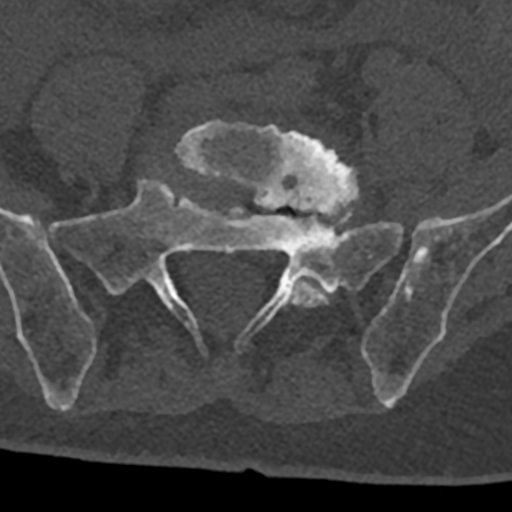
CT including the spine, one axial slice; slice 166 of 797 in the series (ordered by position); reconstruction kernel Br40s/3; 120 kVp; bone window (W 1800 / L 400 HU); 0.5 mm slice thickness; 512 × 512 image matrix. Patient: male, 74 years. Case-level facts recorded for this patient, not image findings: primary cancer: renal; vertebrae with lytic lesions (as recorded): T10, L1, L2, L3, L4, L5.
Annotated regions visible in this slice (semi-automatic segmentation, software-assisted and operator-edited):
- L5 vertebra: bounding box [x1, y1, x2, y2] px = [174, 121, 360, 308]